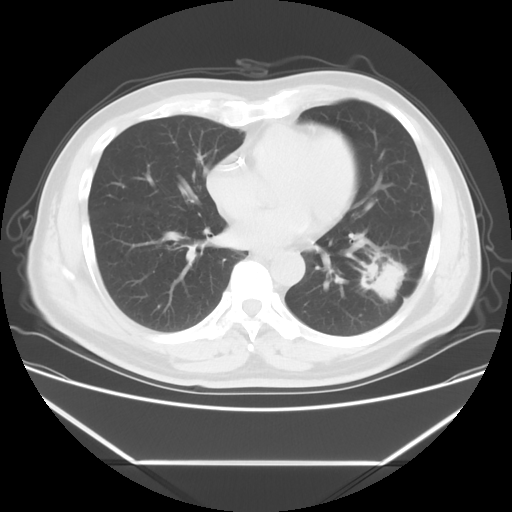
Chest CT, one axial slice; lung window (W 1500 / L -600 HU); 512 × 512 image matrix, field of view 384 × 384 mm. Patient: male, 53 years. From the clinical record (not read from this slice): clinical TNM (as recorded): T1c N0 M0.
Outlined on this slice (bounding box drawn by a radiologist):
- lung tumour (recorded histology: adenocarcinoma): bounding box (x1, y1, x2, y2) in pixels: (355, 250, 416, 310)